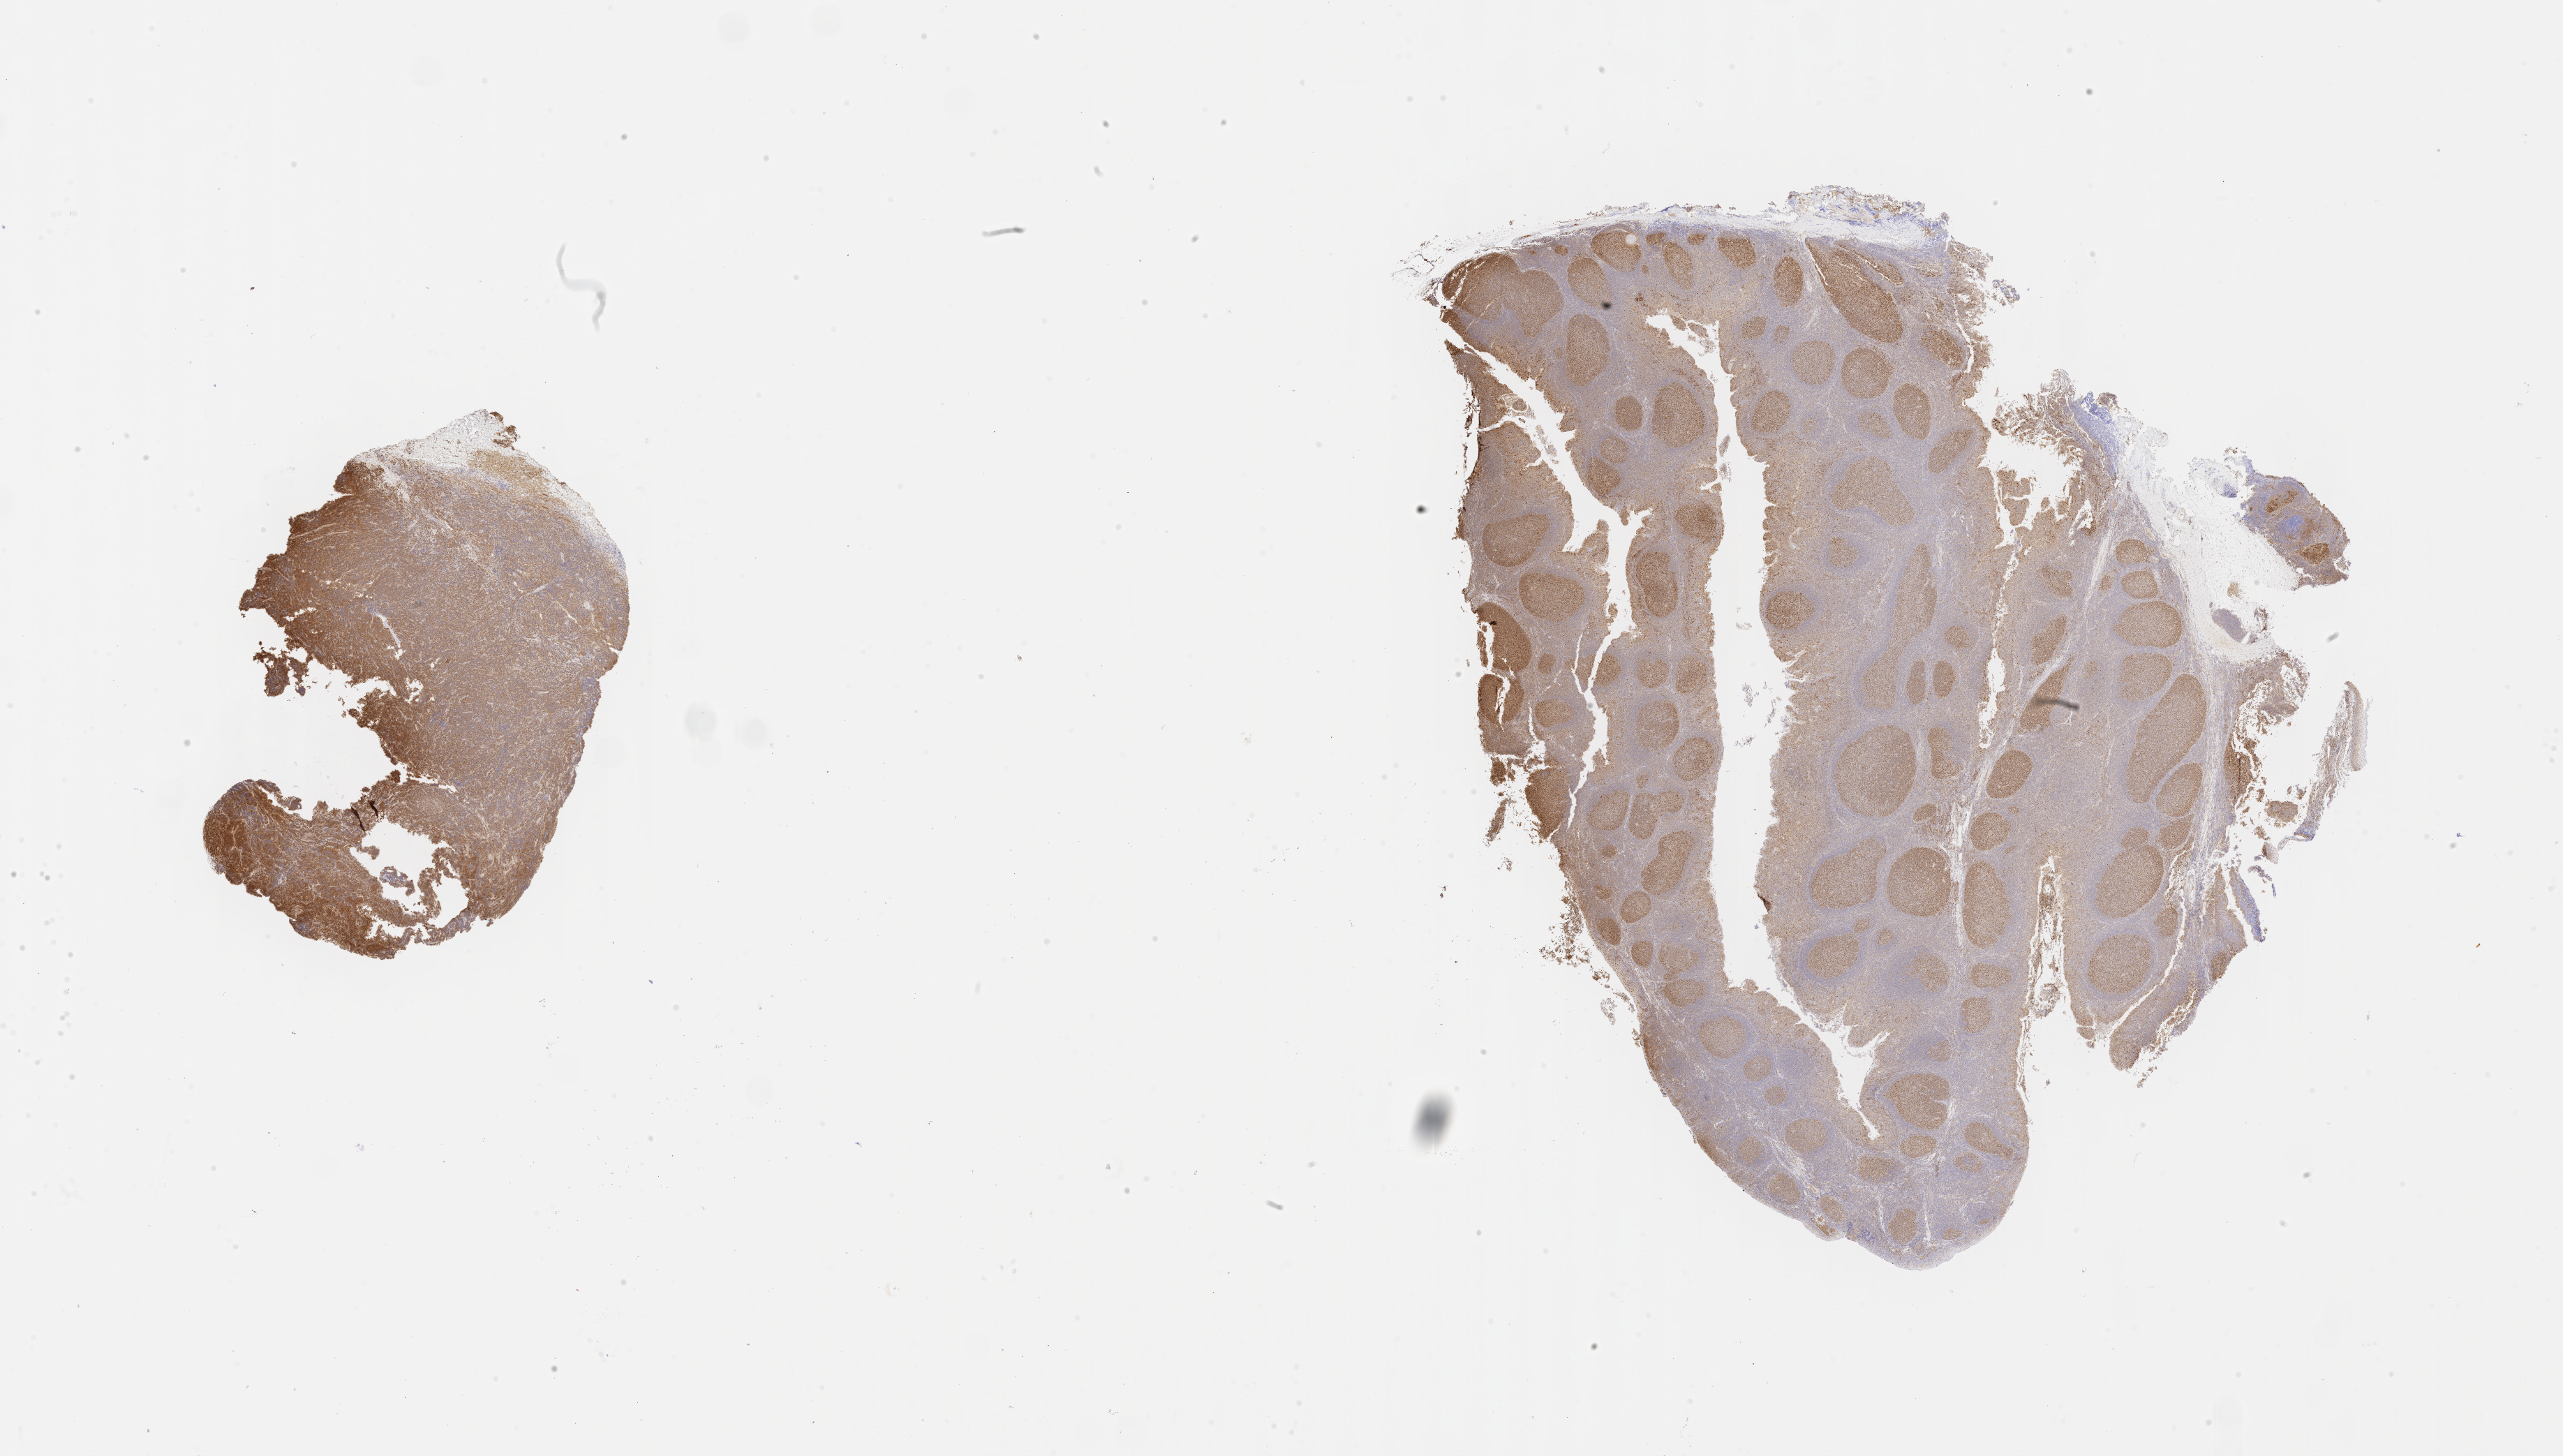
Immunohistochemistry (IHC) whole-slide image stained for BCL6, shown as a low-resolution overview of the whole scanned area (about 29.7 x 16.9 mm), specimen: tumor tissue, anatomic site: mandible. Patient: female, age at initial diagnosis 7 years.
Diagnosis: Burkitt lymphoma, NOS.